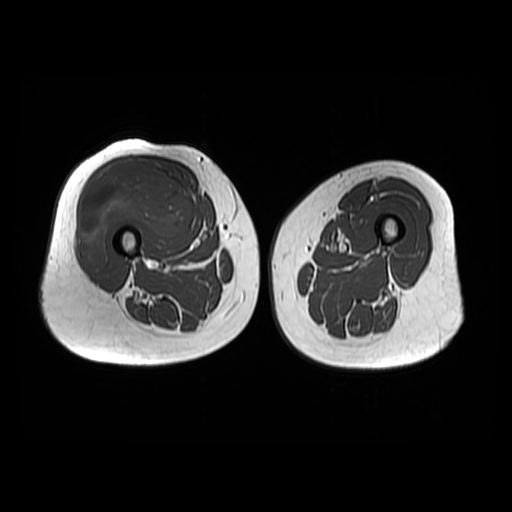
MRI of an extremity soft-tissue mass, one axial slice; position 24 of 48 along the scan axis; 6 mm slice thickness; 512 × 512 image matrix, field of view 440 × 440 mm. Female patient. Case-level facts recorded for this patient, not image findings: histological type: pleiomorphic undifferentiated sarcoma; grade: high; site of the primary tumour: right quadricep.
Structures marked on this image (manually delineated by an expert):
- gross tumour volume including surrounding oedema: box from (x=79, y=161) to (x=194, y=272) px
- gross tumour volume (mass): (x=79, y=161)–(x=194, y=272)